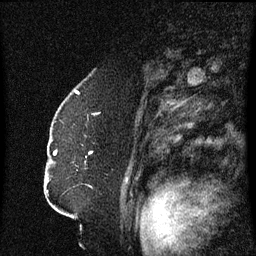
Breast MRI (dynamic contrast-enhanced), one sagittal slice. Position 45 of 60 along the scan axis. Dynamic contrast-enhanced series, image 2 of 3 at this slice position (ordered by acquisition). 1.5 T. TE 4.2 ms, TR 8.4 ms. 256 × 256 image matrix, field of view 200 × 200 mm. Patient: female, 52 years. From the clinical record (not read from this slice): setting: breast cancer imaged before/during neoadjuvant chemotherapy; receptor status: HR-positive, HER2-negative.
Annotated regions visible in this slice (semi-automatically segmented with operator editing):
- analysis volume of interest (the breast-tissue region the enhancement analysis was run in; not a lesion): bounding box <49,124,125,191> (left, top, right, bottom; pixels)
- tumour enhancement mask (voxels above the 70 % enhancement threshold inside the analysis volume of interest): <54,152,92,155>